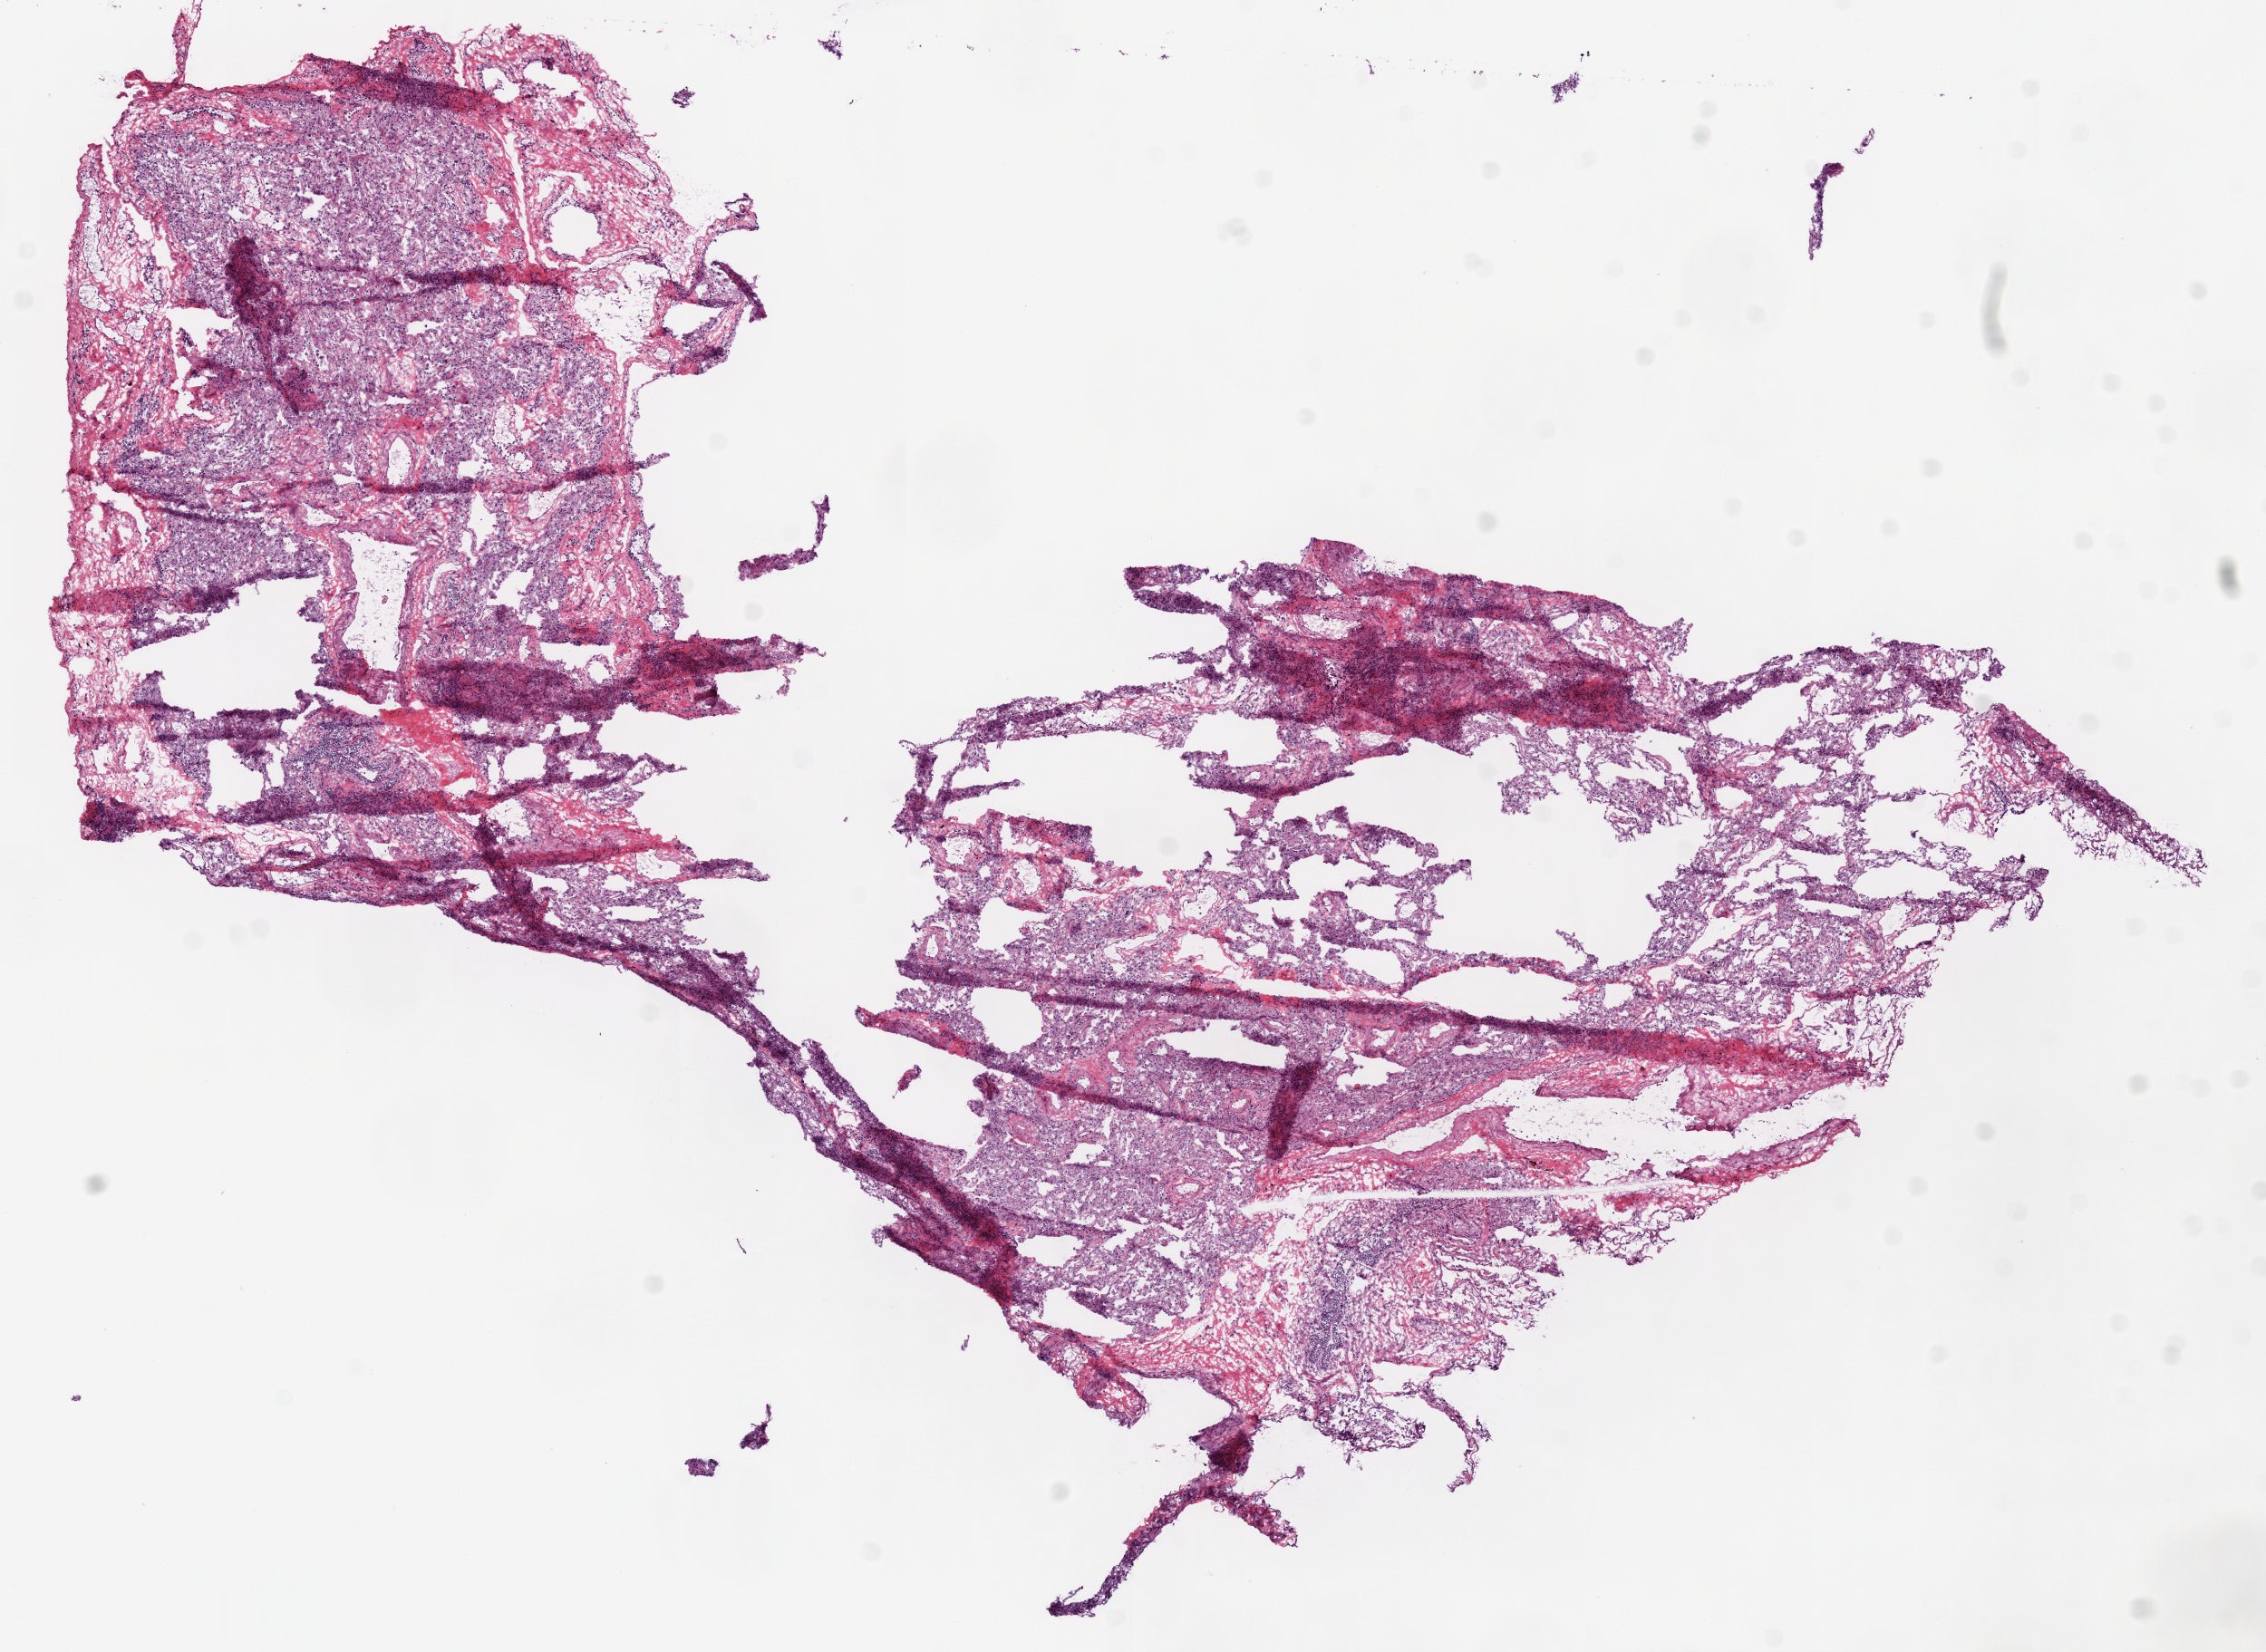
Digitized H&E tissue section (whole slide), shown as a low-resolution overview of the whole scanned area (about 10.0 x 7.3 mm, from a 20x scan). Frozen section from the bottom of the tissue portion. Lung, solid tissue normal (non-tumour tissue) sample. Male patient; age at initial diagnosis 66 years.
* this section: solid tissue normal sample (biorepository sample class)
* patient diagnosis: Squamous cell carcinoma, NOS (upper lobe, lung)